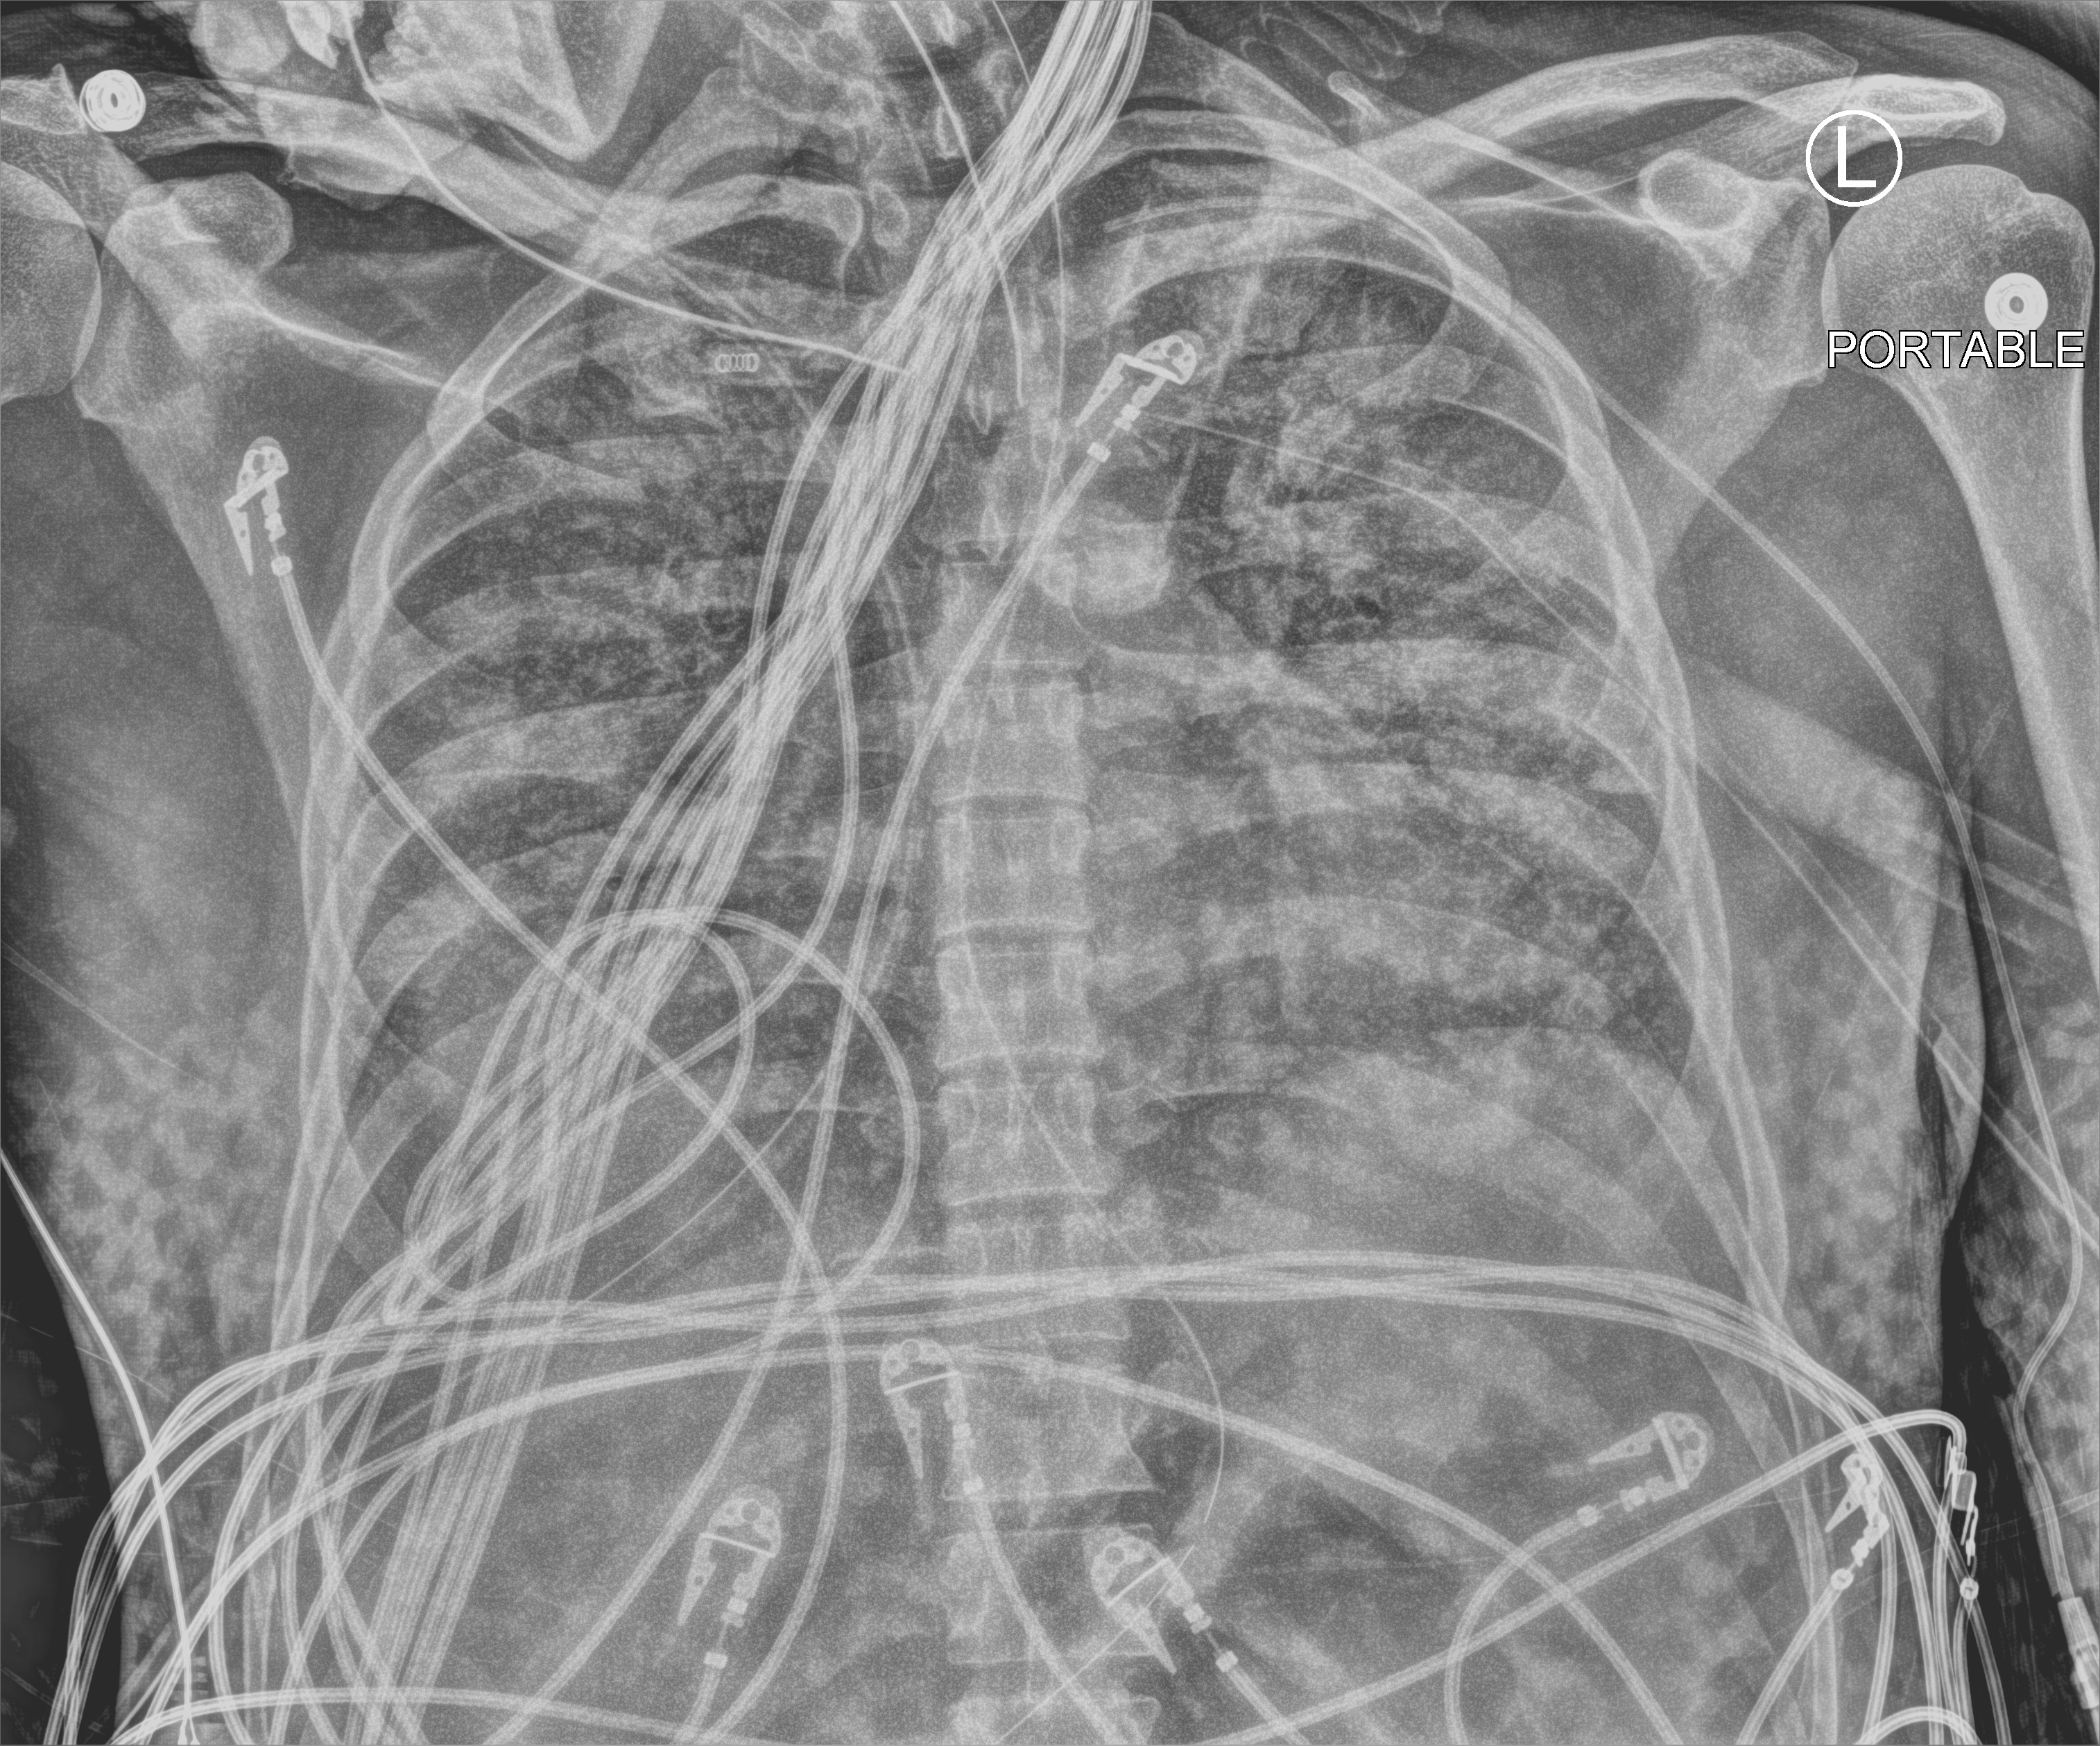
Bedside chest radiograph (computed radiography), anteroposterior (AP) projection. Male patient hospitalised with COVID-19, age 18–59 years.
Admission-level facts for this patient (not findings on this image; timing relative to this image not recorded):
- mechanically ventilated during this hospital stay: yes